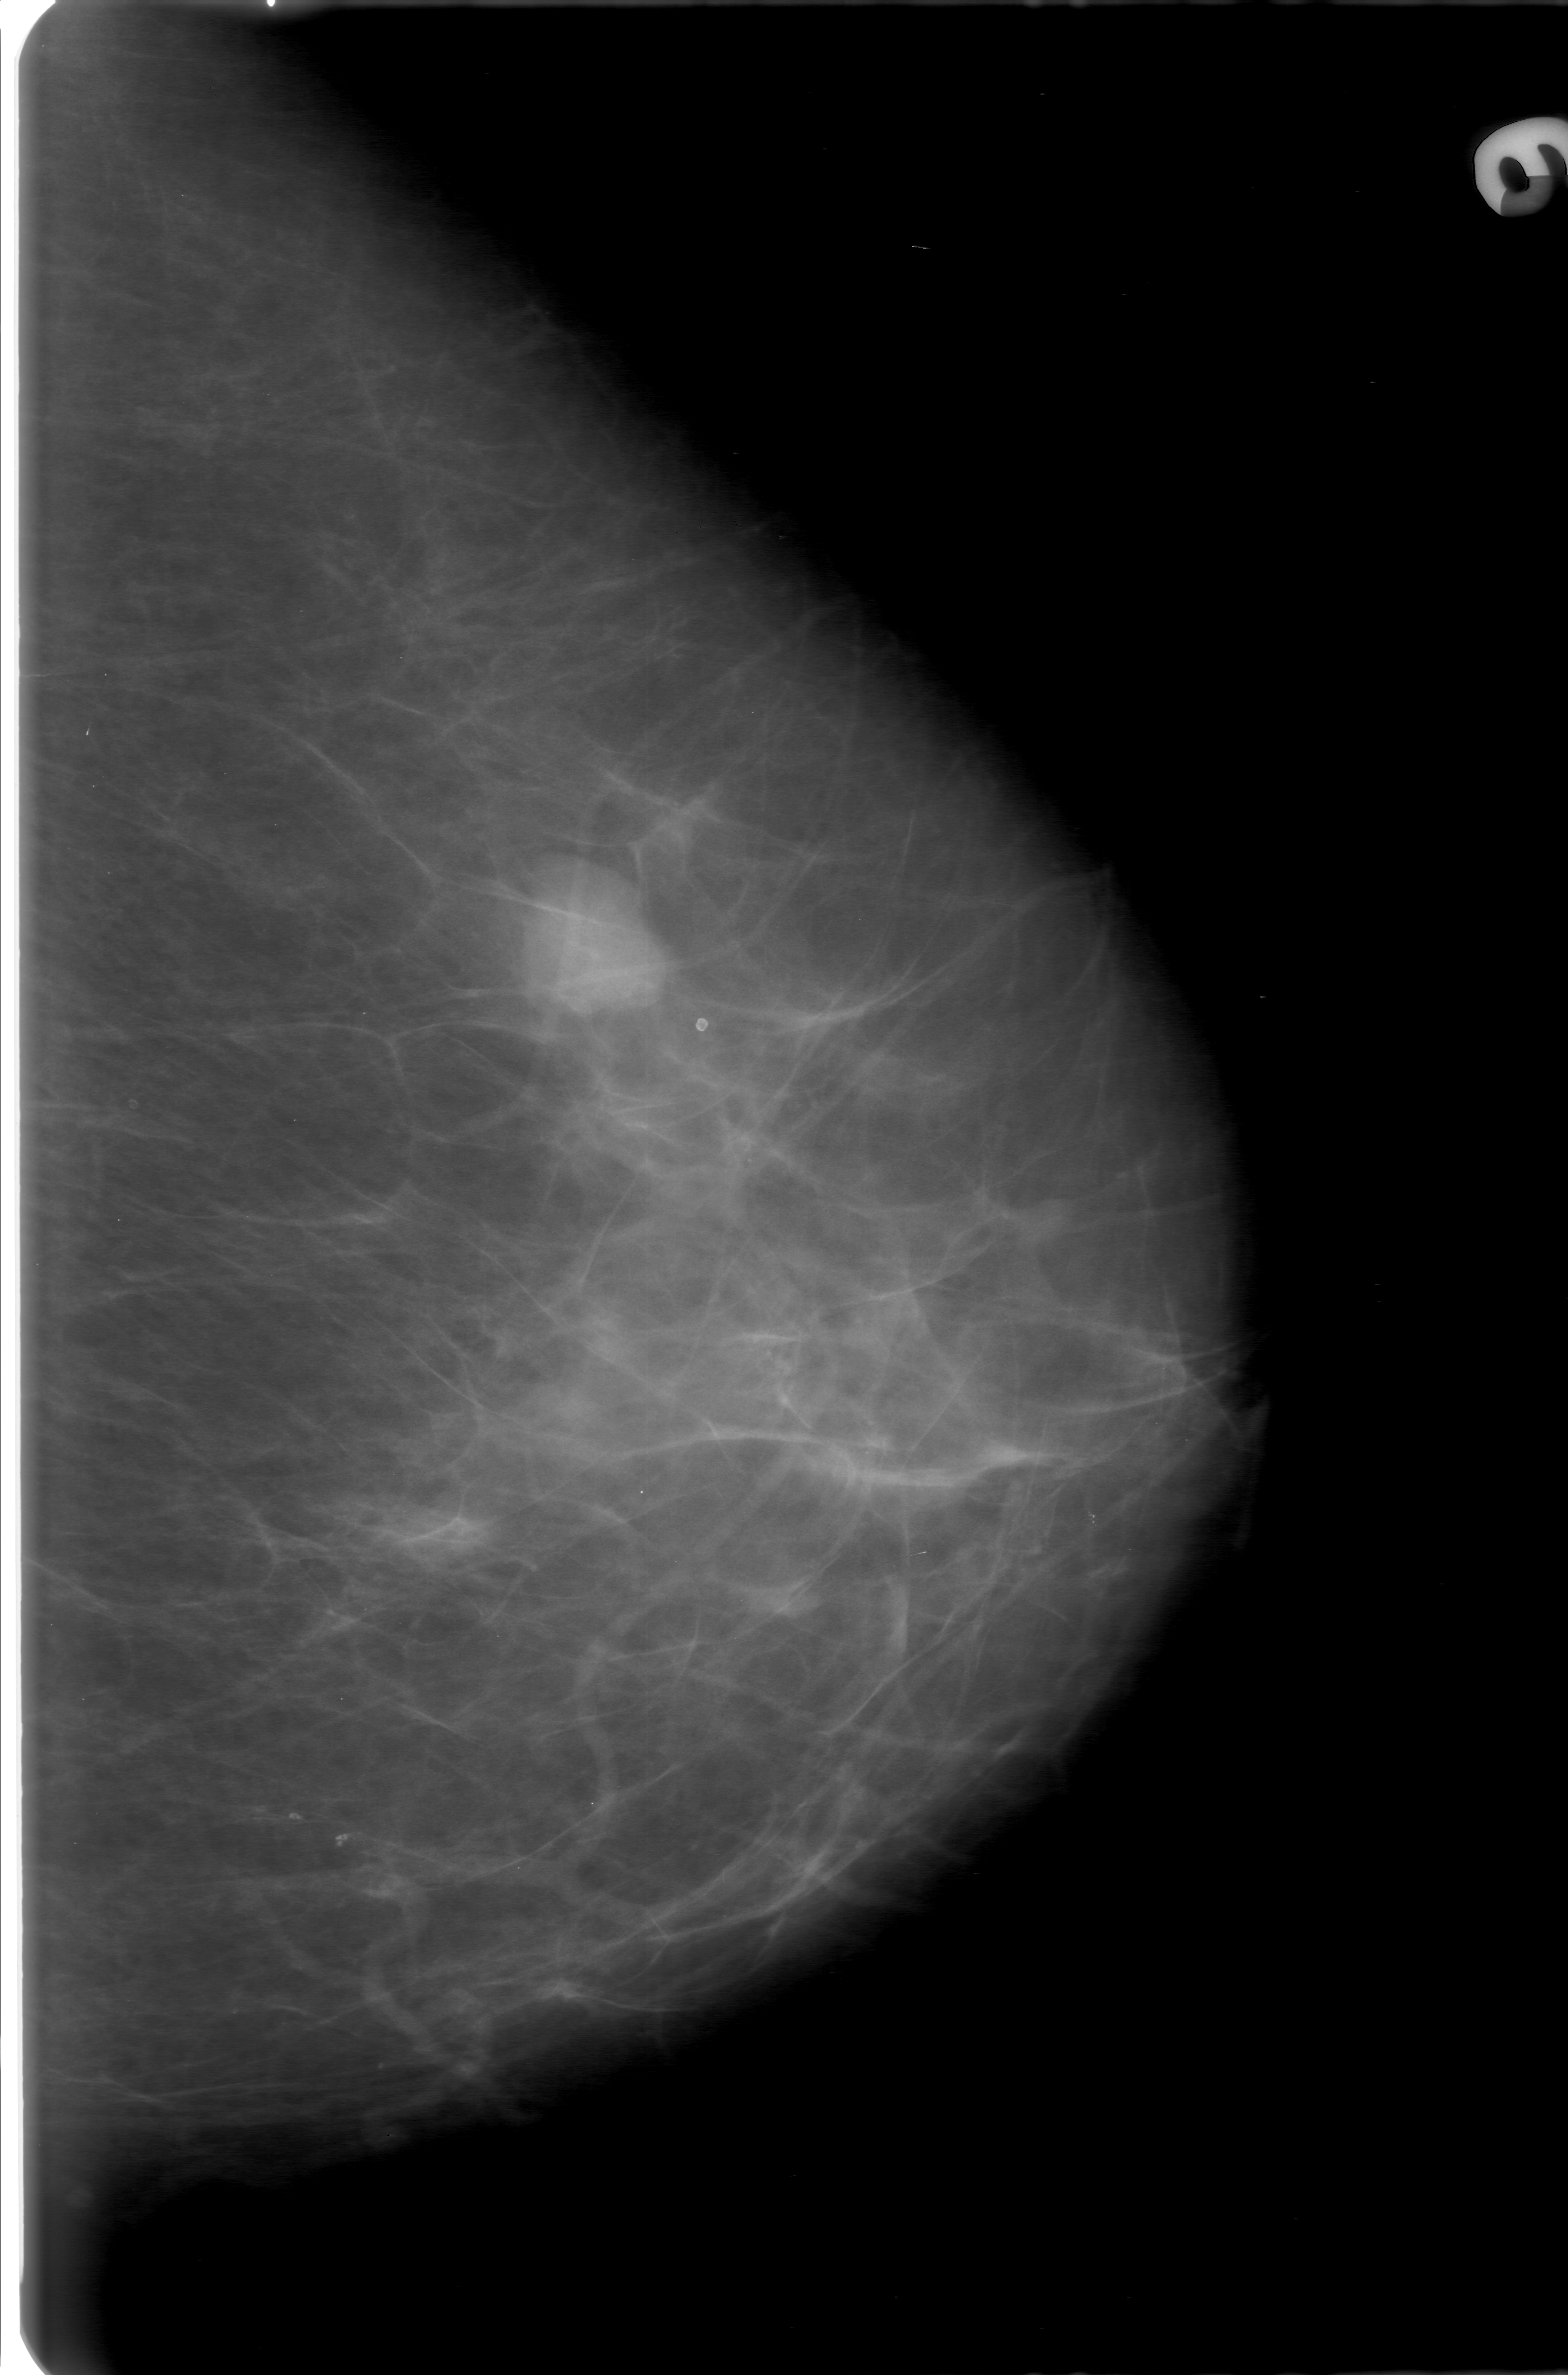
Digitized screen-film mammogram; left breast; craniocaudal (CC) view; breast composition: almost entirely fatty (BI-RADS density category 1 of 4); 1568 × 2375 image matrix.
Expert-marked regions of interest on this film, with their recorded descriptors:
- mass, shape lobulated, margins circumscribed; BI-RADS assessment category 0; subtlety rating 5 on a 1 (subtle) to 5 (obvious) scale; pathology (as recorded): benign: bounding box [x1, y1, x2, y2] px = [510, 878, 685, 1054]